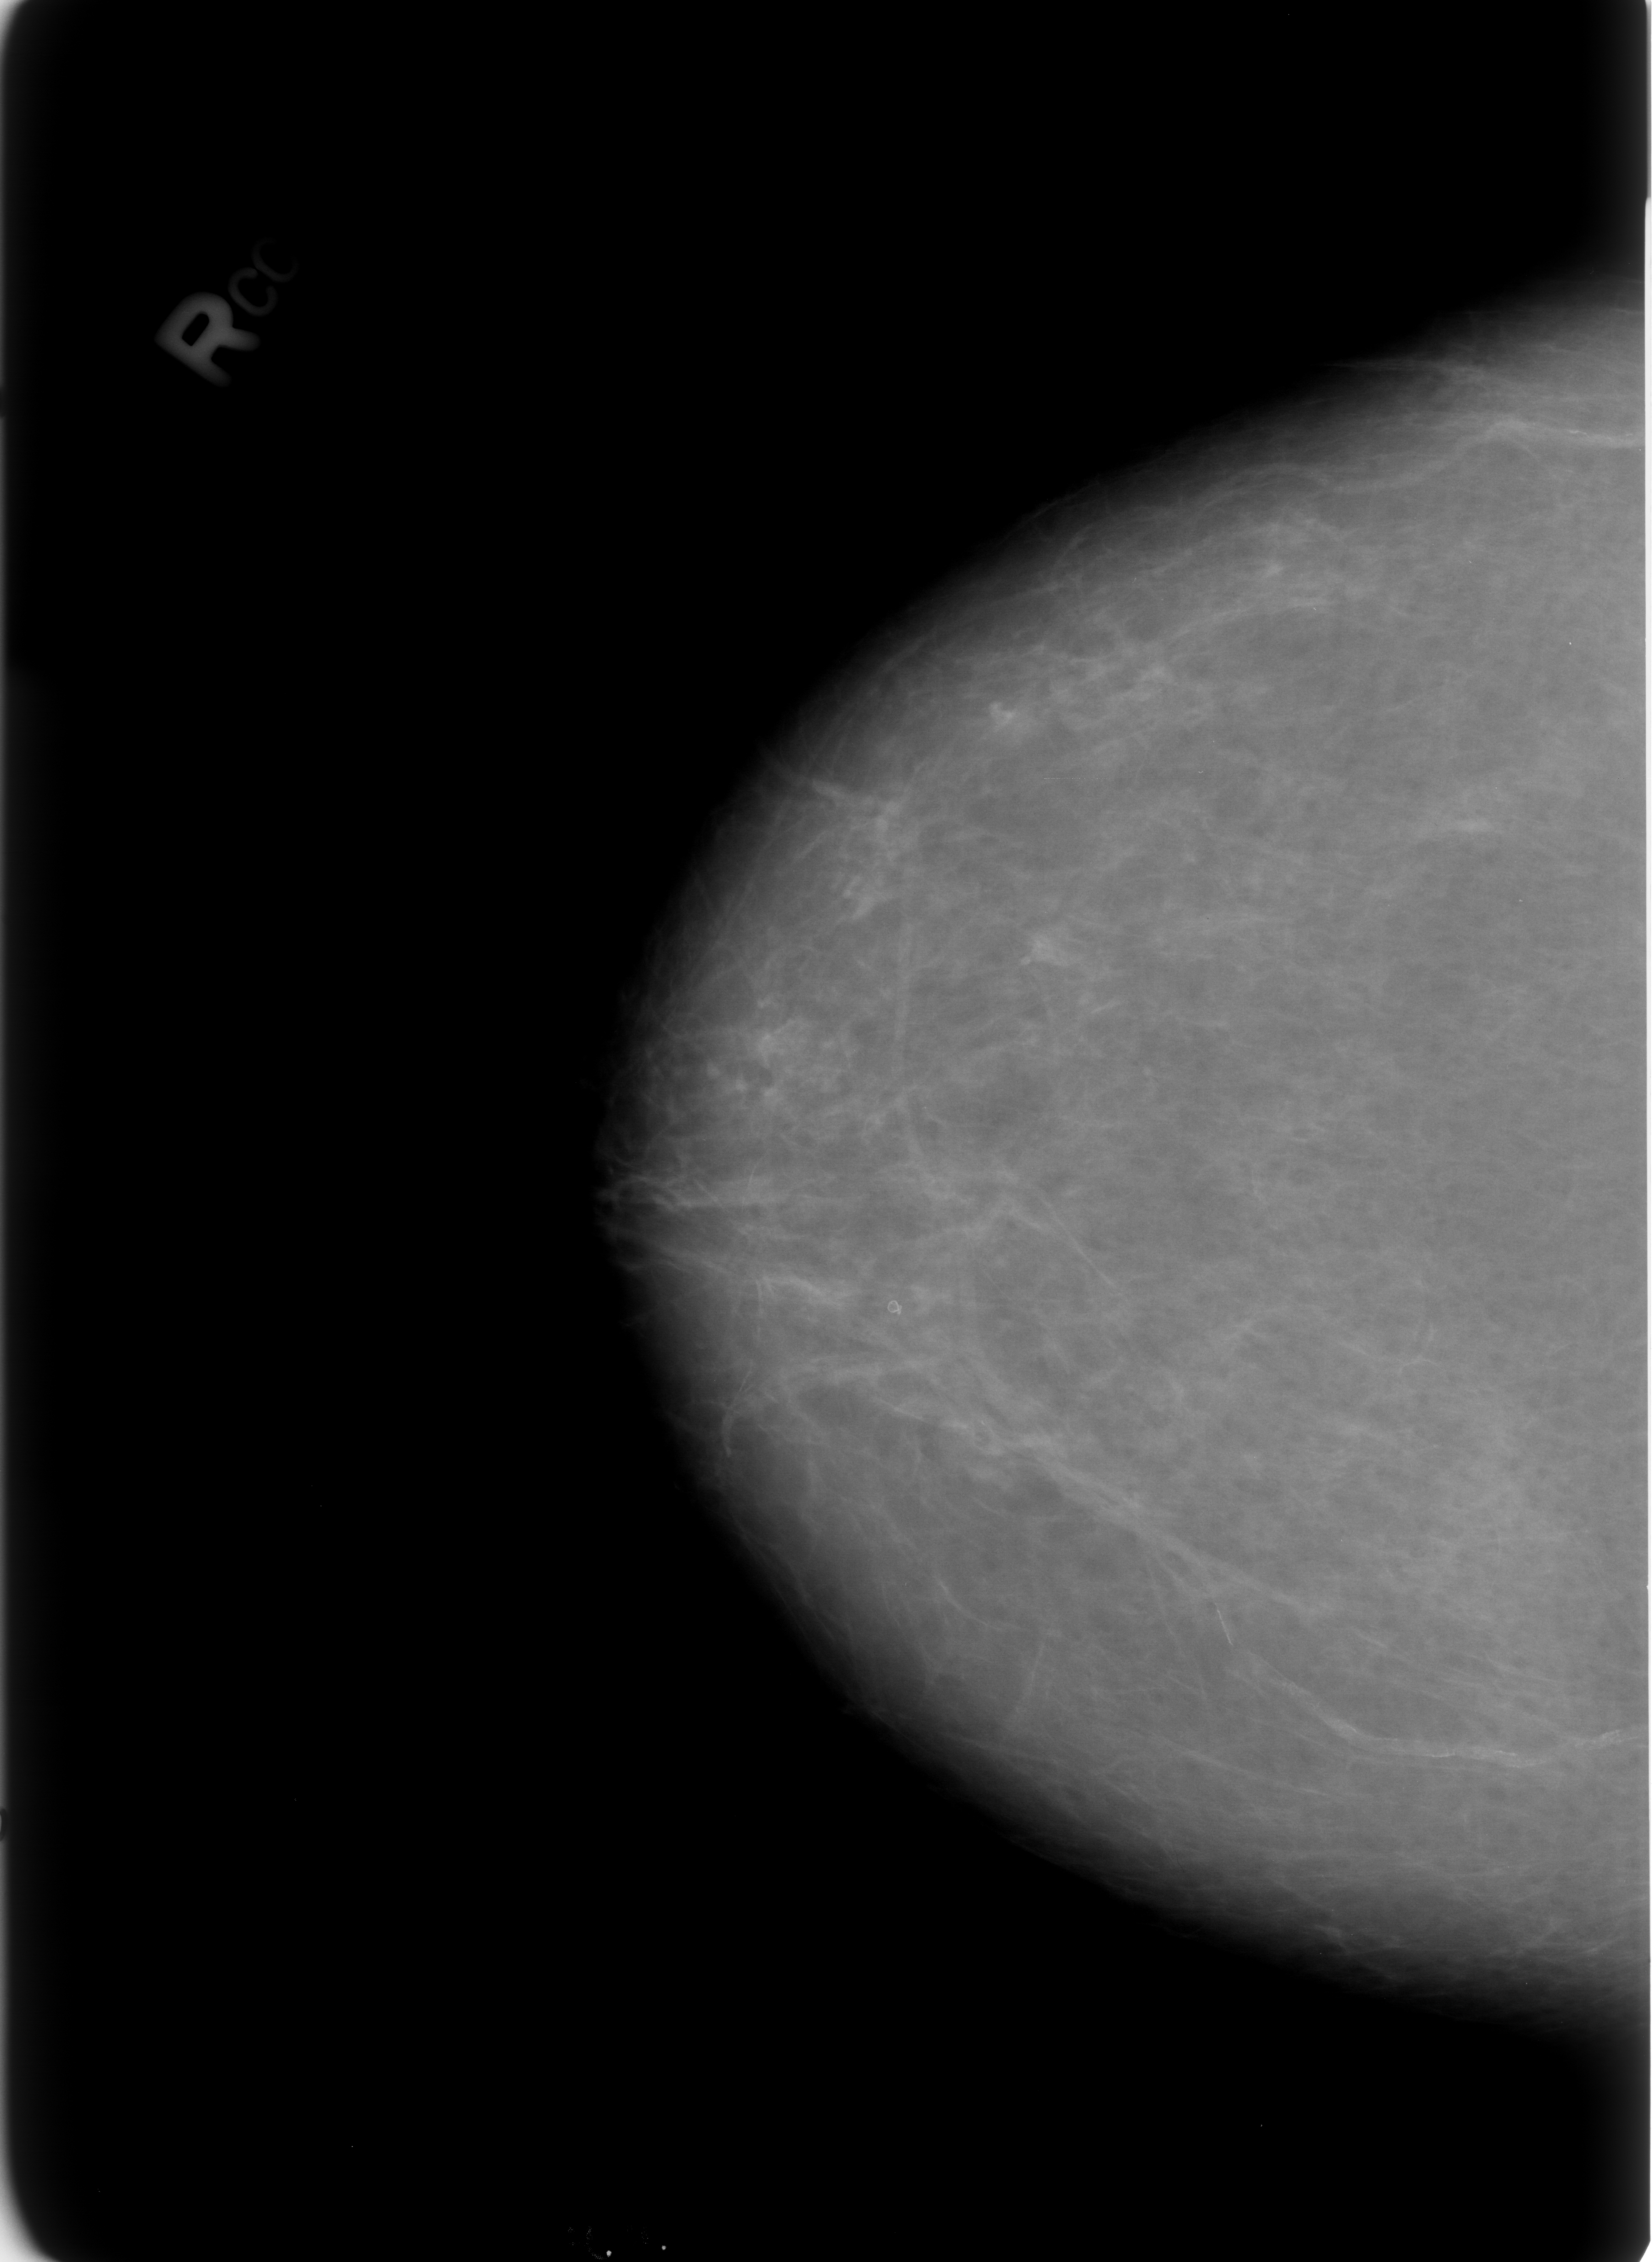
Scanned film-screen mammogram; right breast; CC view; breast composition: almost entirely fatty (BI-RADS density category 1 of 4).
Marked abnormality: calcifications, morphology lucent centered; BI-RADS assessment category 2; benign without callback (not worked up further).